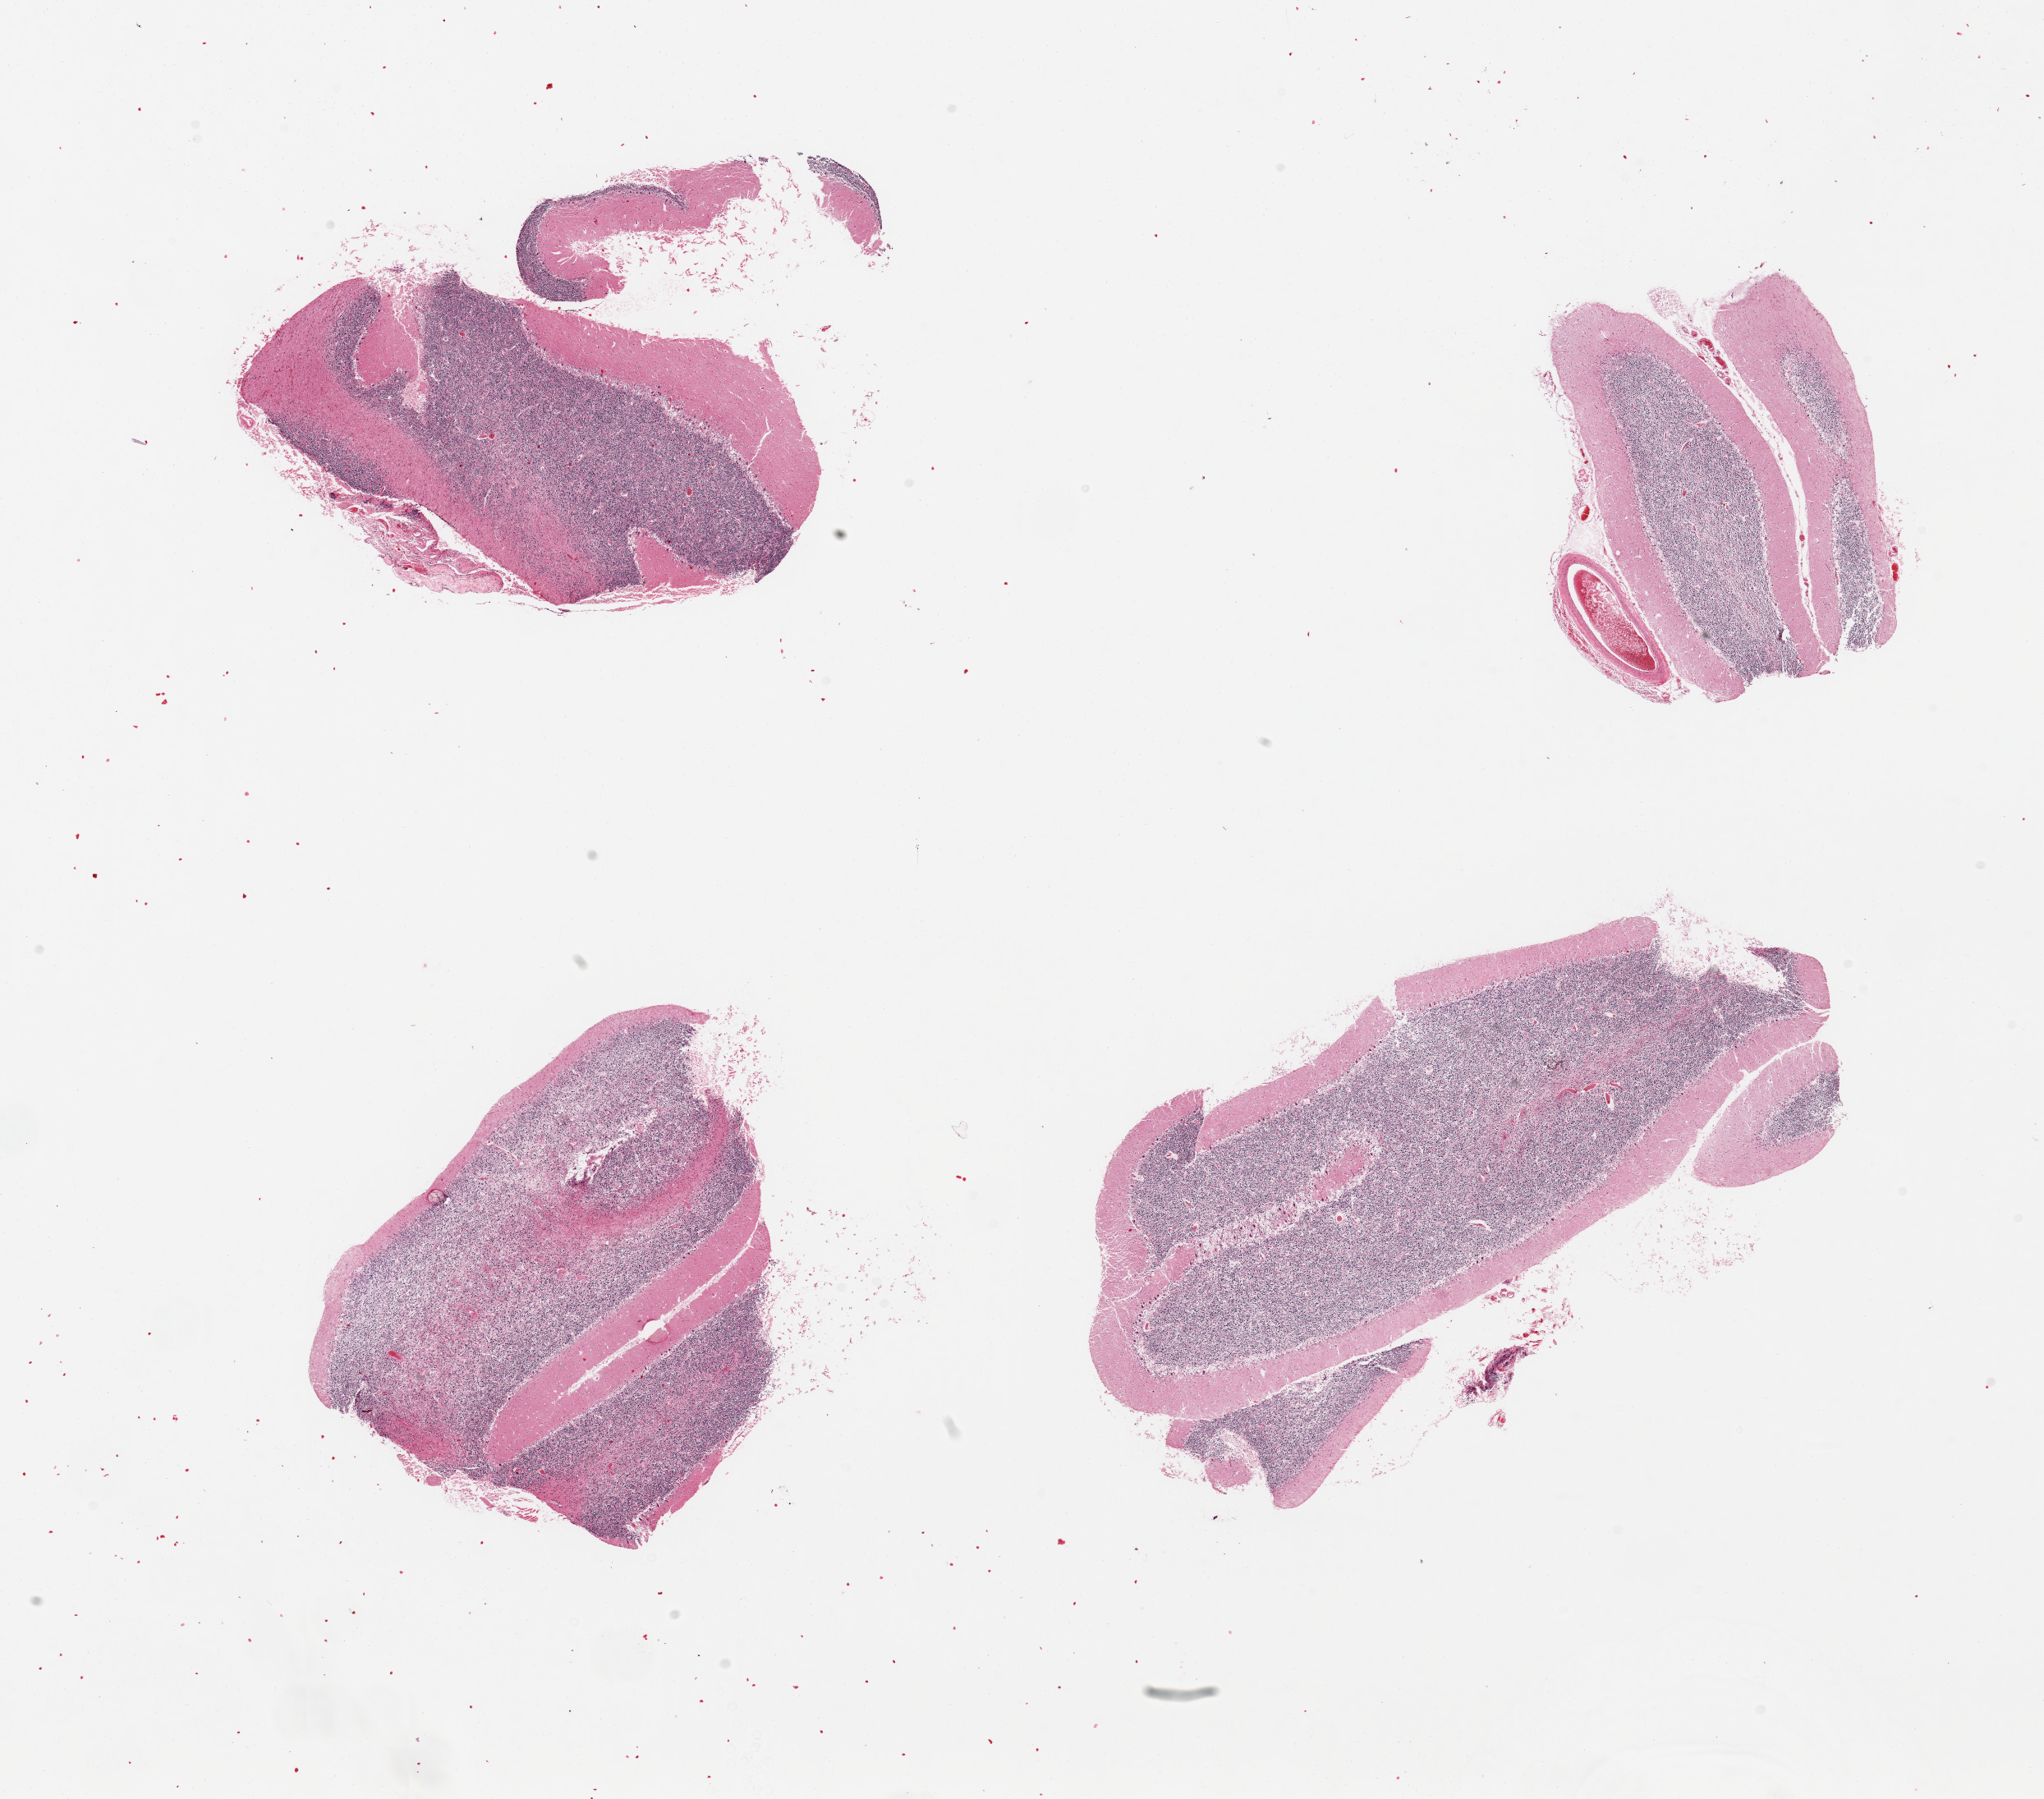
Whole-slide image, hematoxylin and eosin (H&E) stain — a low-resolution overview of the entire scanned area, about 19.7 x 17.3 mm (acquisition: 20x scan); PAXgene-fixed, paraffin-embedded tissue; target tissue: cerebellum; donor tissue sample. Male donor.
Pathologist's review note for this sample: 4 pieces; some suggestion of hypoxic change, portion of meninges.